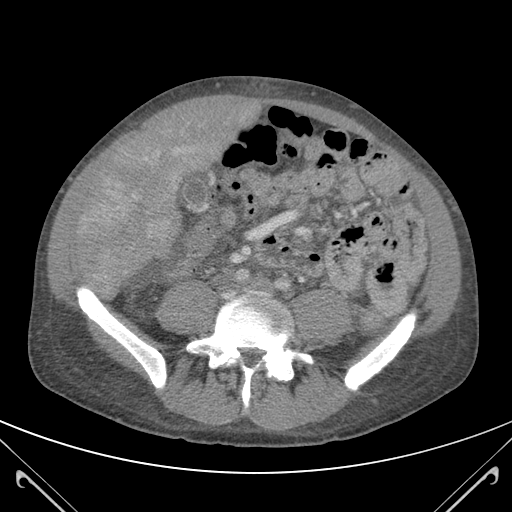
Contrast-enhanced abdominal CT (liver protocol), one axial slice. Position 29 of 118 along the scan axis. 120 kVp. Soft-tissue window (W 400 / L 40 HU). 512 × 512 image matrix. Case-level facts recorded for this patient, not image findings: diagnosis: hepatocellular carcinoma (patient treated with transarterial chemoembolisation; whether this scan precedes or follows treatment is not stated here); TNM stage (as recorded): Stage-IIIB; Child-Pugh class: A; tumour nodularity: uninodular.
Structures marked on this image (semi-automatically segmented with operator editing):
- mass: bounding box (x1, y1, x2, y2) in pixels: (70, 95, 242, 282)